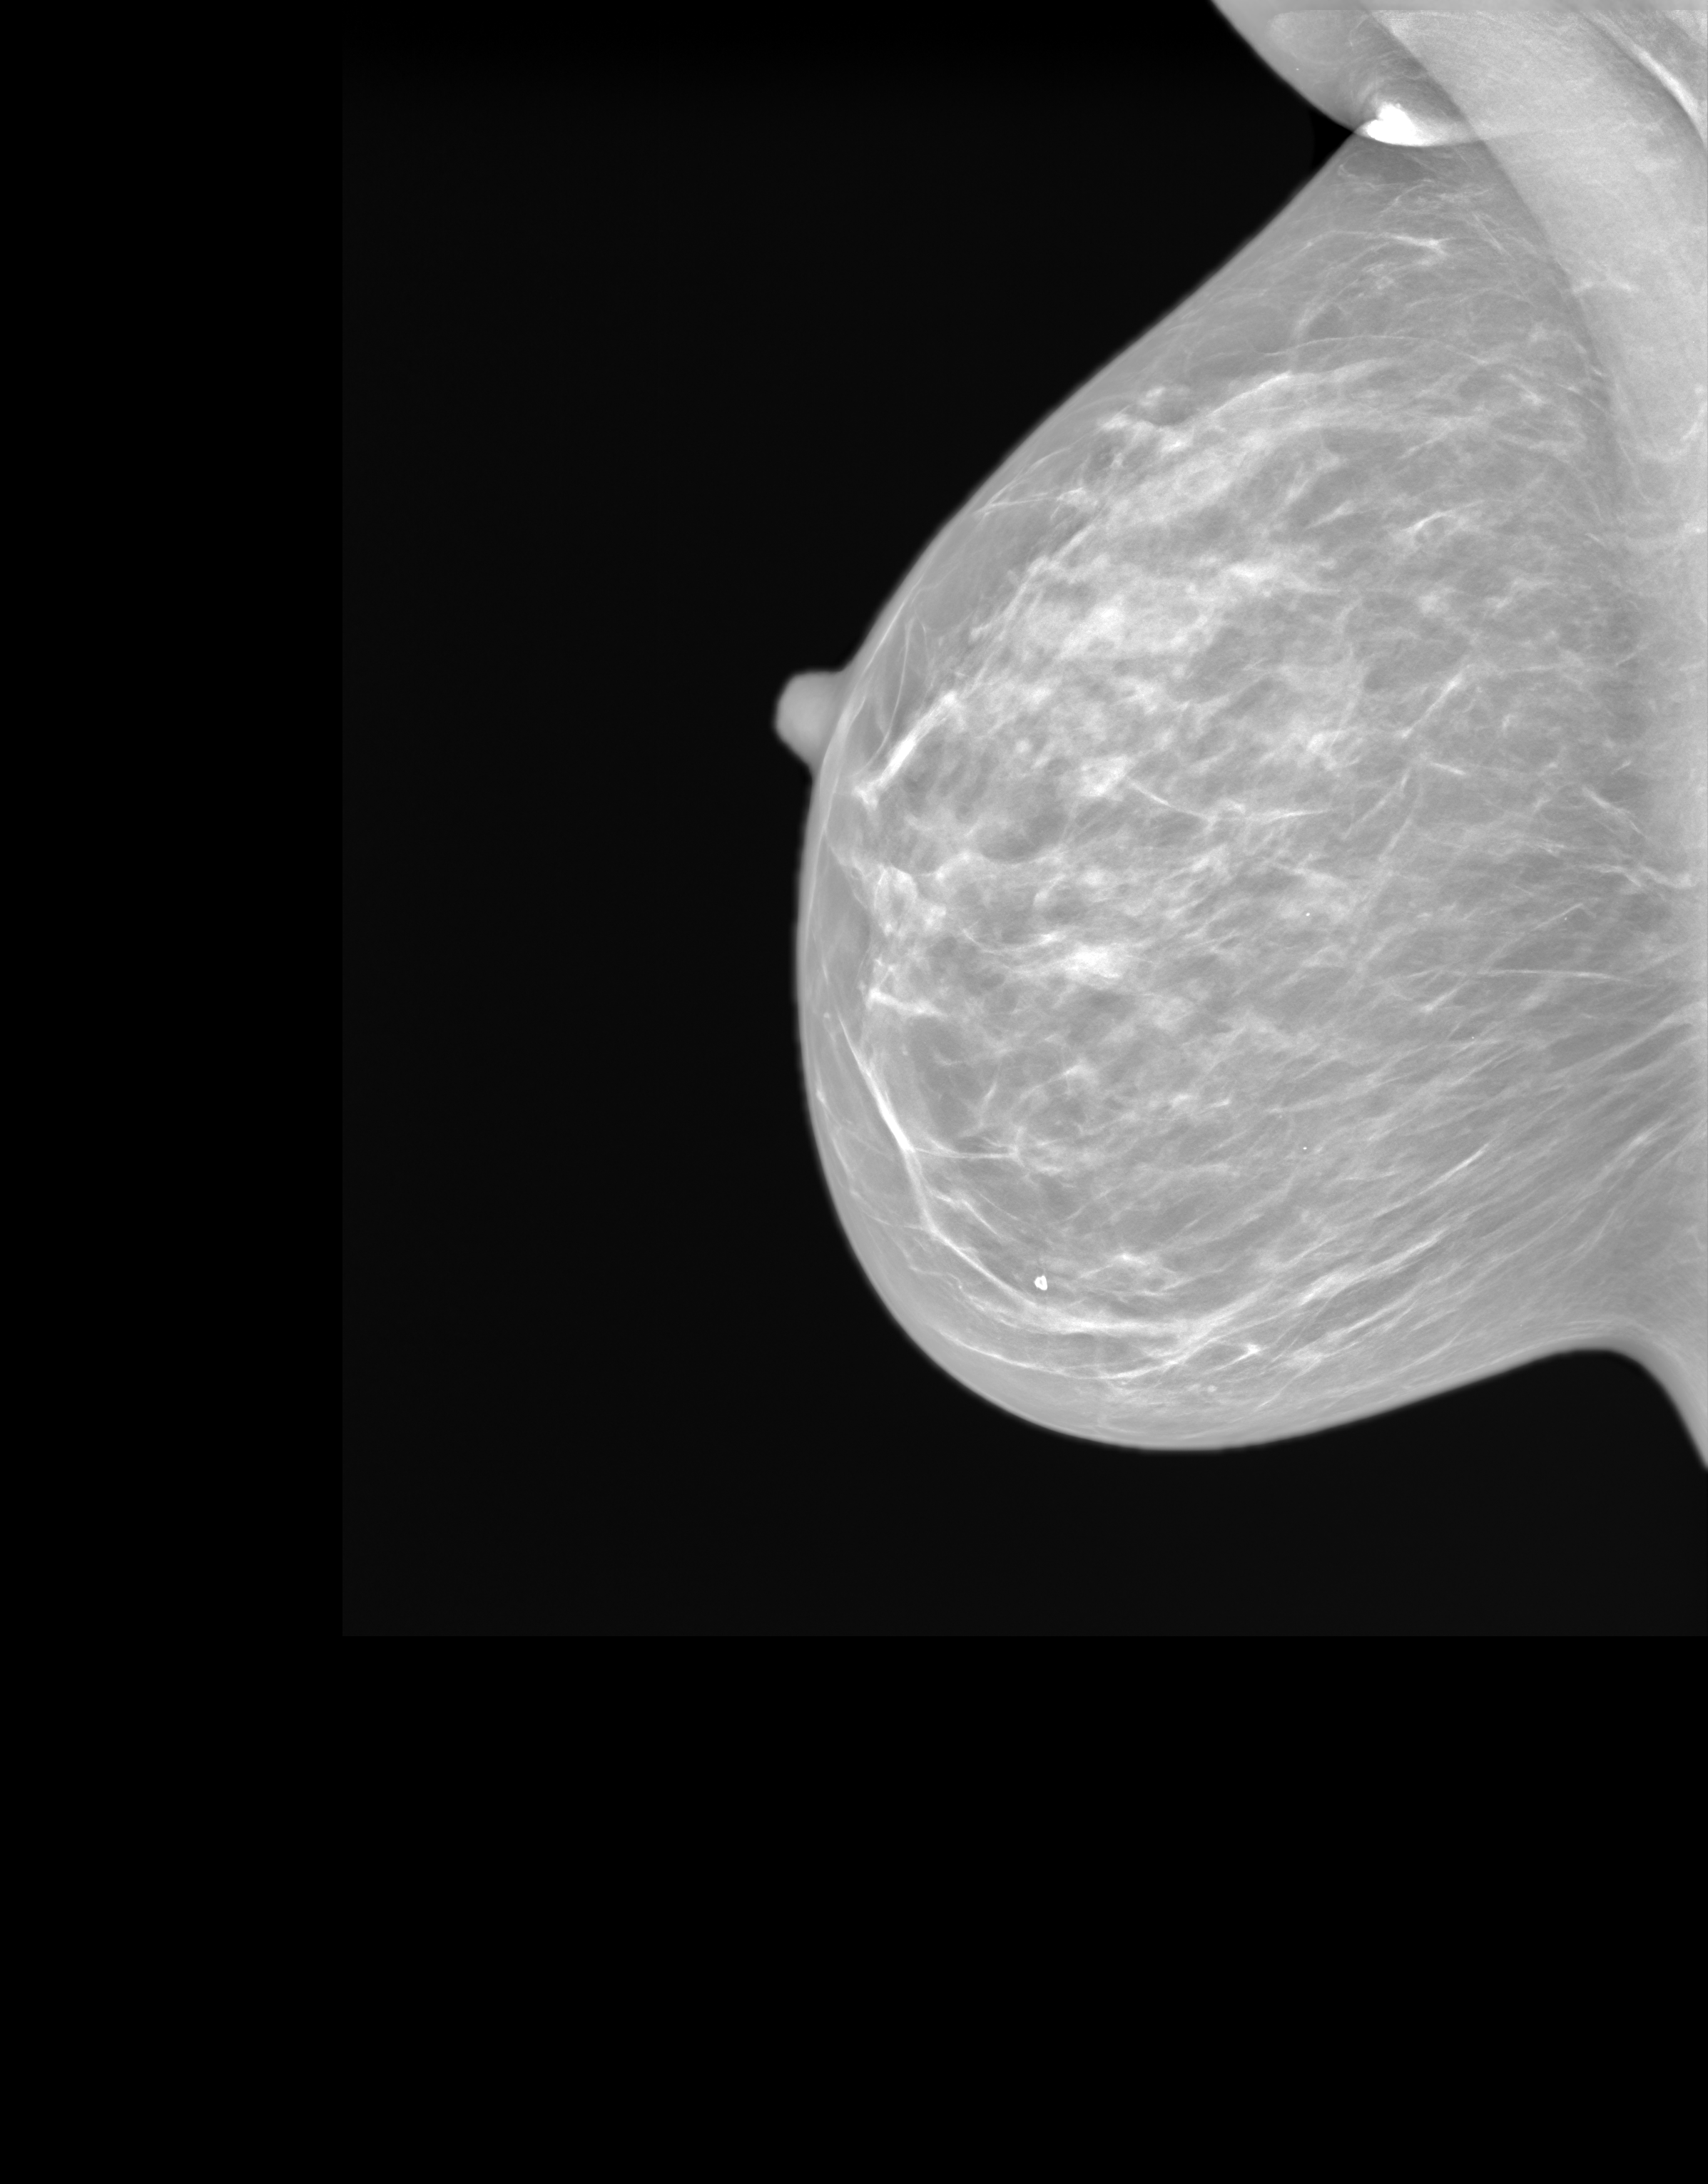
Screening examination. Patient: female, 56 years.
Image type: synthesized 2-D view from tomosynthesis. Breast: right. Projection: MLO view.